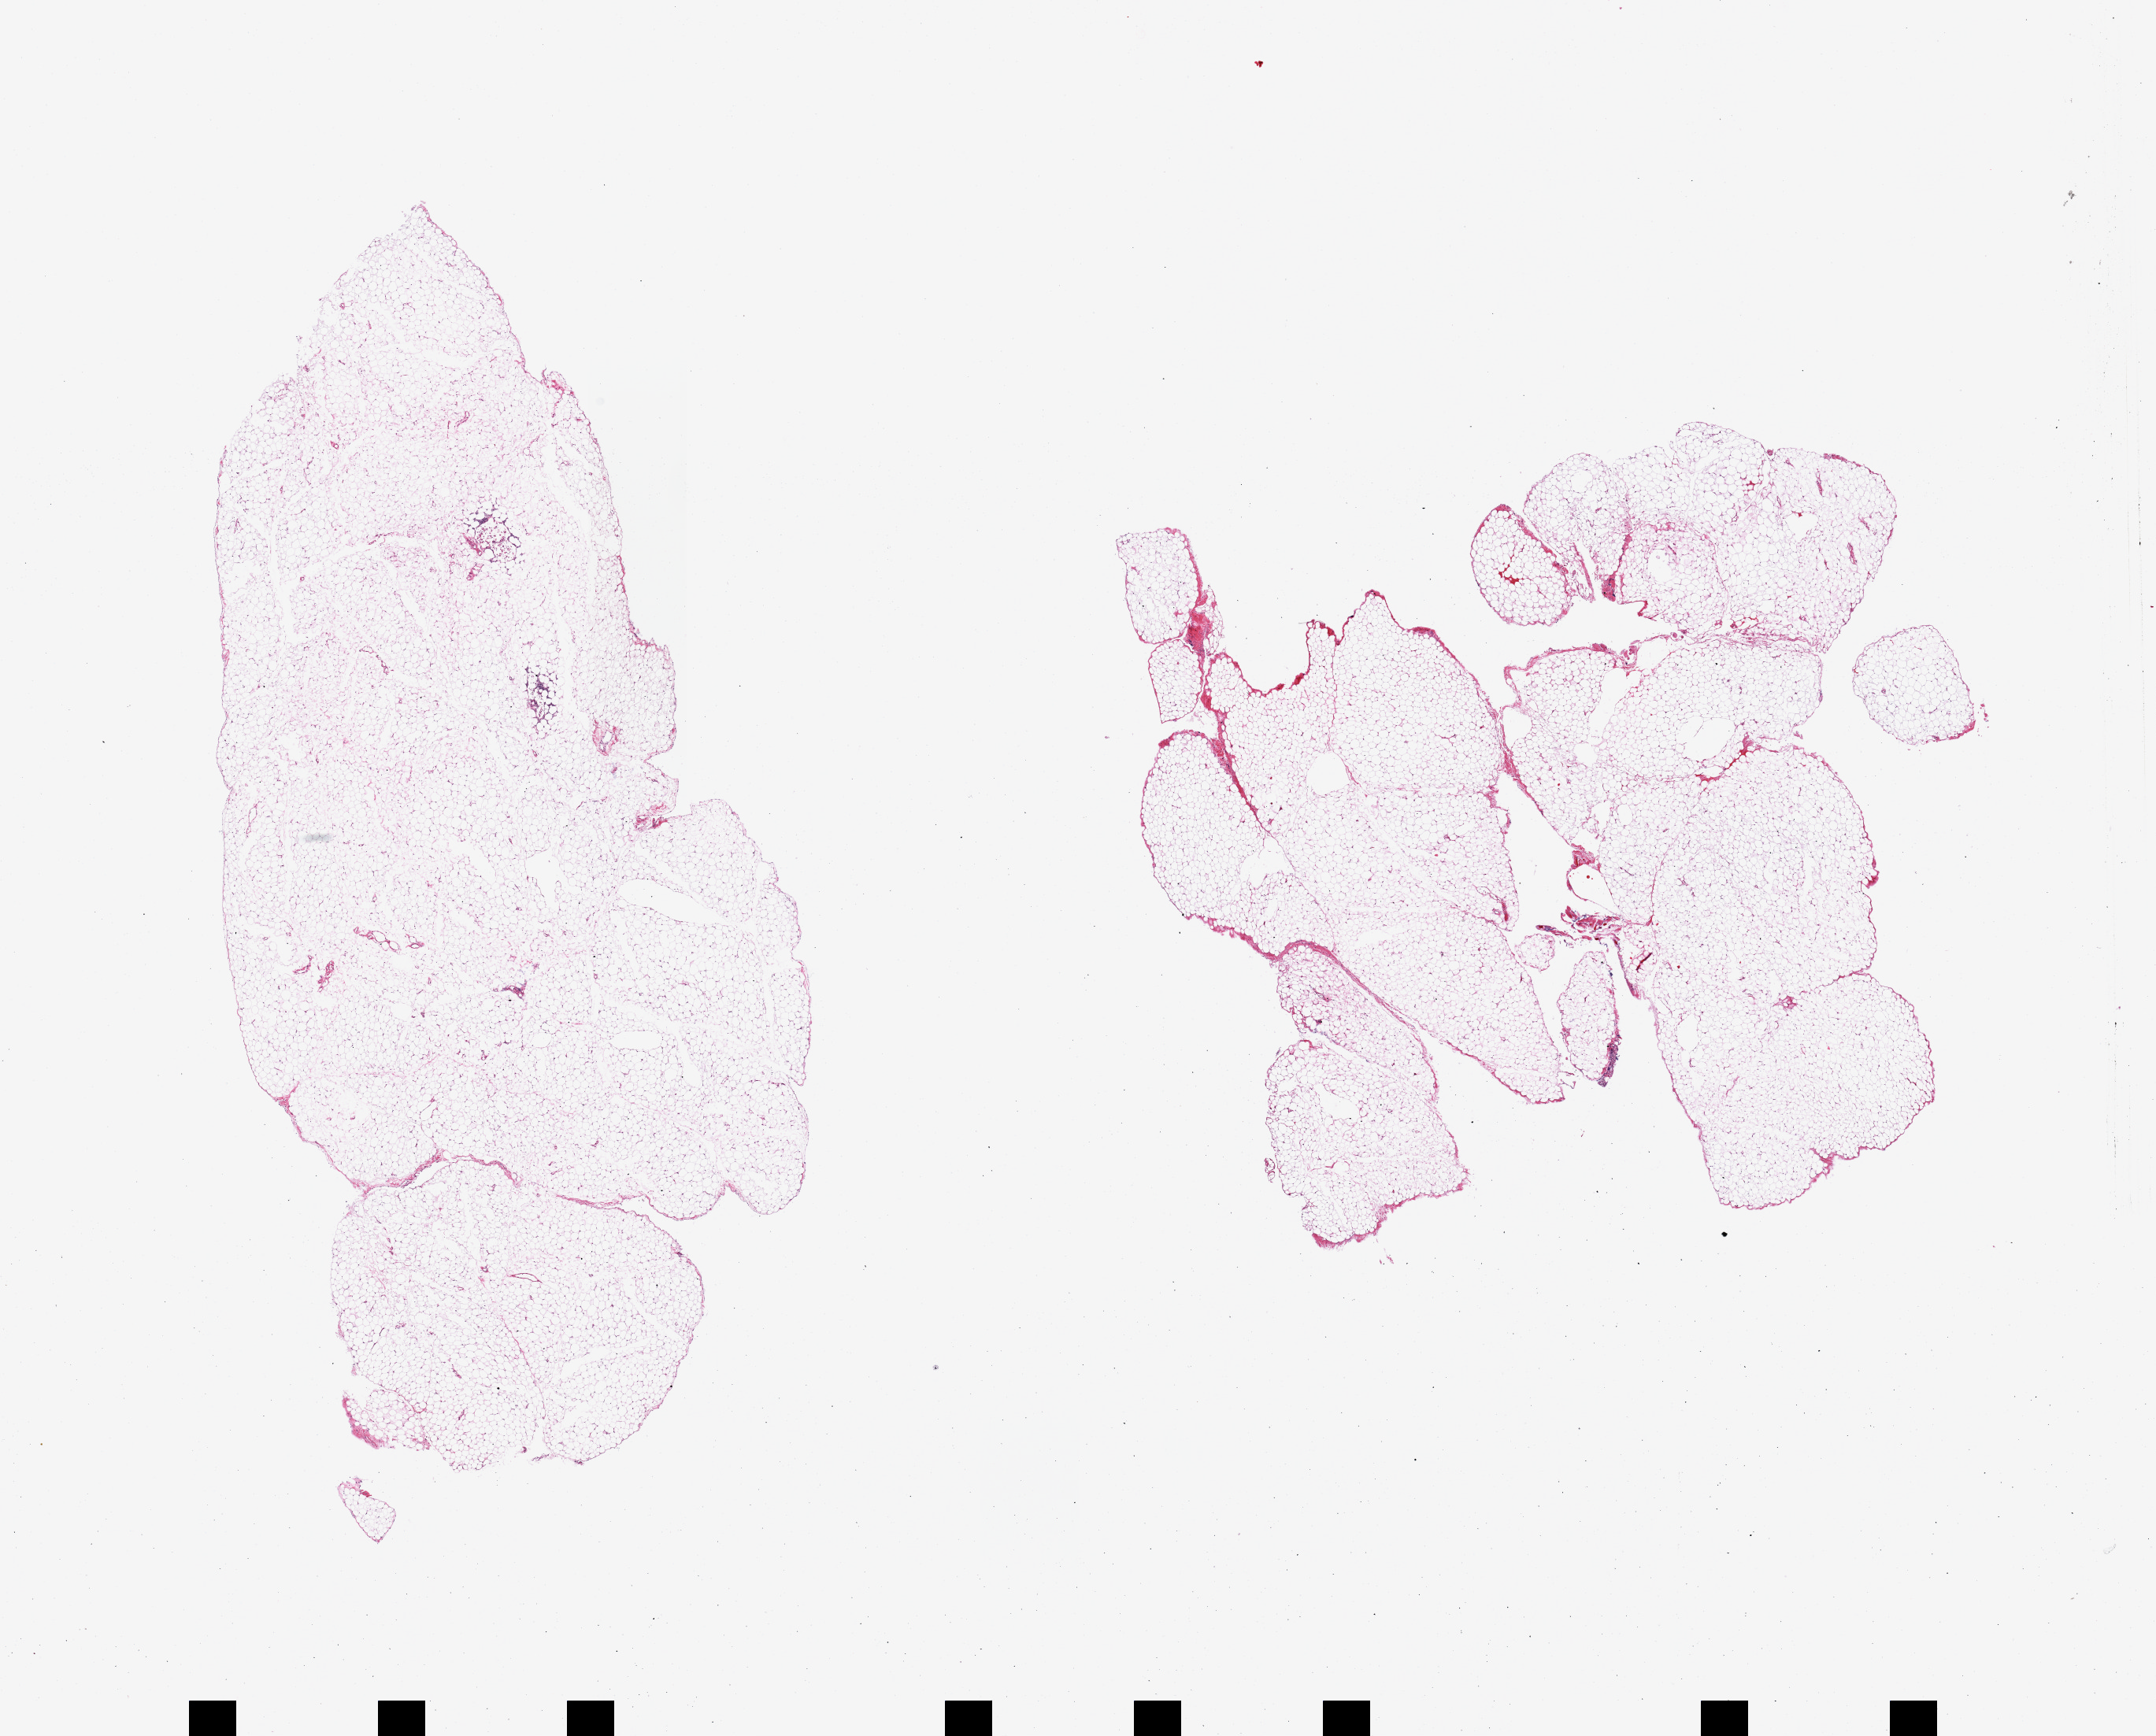
Whole-slide image, haematoxylin and eosin stain, low-resolution overview of the scanned area, about 21.7 x 17.4 mm, PAXgene-fixed paraffin-embedded (PFPE) section, section of omentum (target tissue), tissue donor sample. Donor sex: male.
• pathologist's review note for this sample: 2 pieces; lobulated mature adipose tissue; minute foci of inflammatory cell infiltration